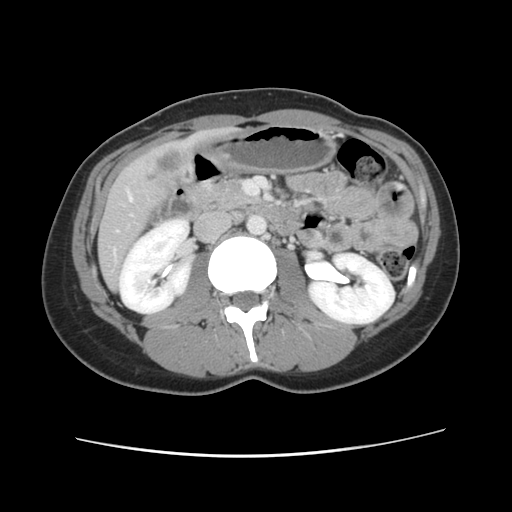
Contrast-enhanced abdominal CT, one axial slice. Position 34 of 134 along the scan axis. Intravenous contrast given. Soft-tissue window (W 400 / L 40 HU). 512 × 512 image matrix, field of view 339 × 339 mm. Female patient, age 33 years. From the clinical record (not read from this slice): diagnosis: colorectal cancer liver metastases, imaged before liver resection; multiple liver metastases: yes; largest metastasis: 4.5 cm; chemotherapy before resection: no.
Annotated regions visible in this slice (manually delineated by an expert):
- hepatic veins: bounding box (x1, y1, x2, y2) in pixels: (128, 193, 132, 199)
- liver: (99, 129, 232, 289)
- planned liver remnant (the part of the liver to remain after resection): (99, 242, 123, 289)
- liver metastasis: (143, 150, 193, 191)